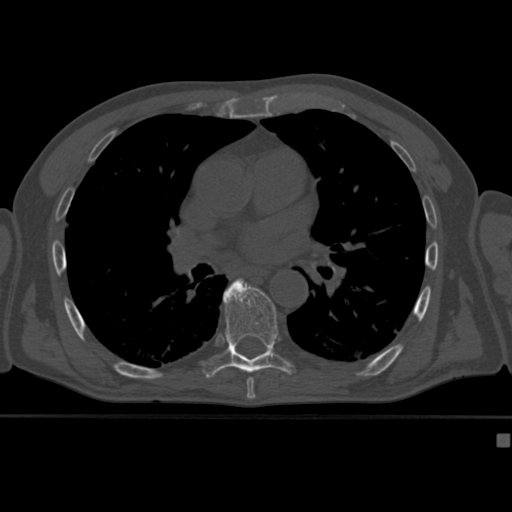
CT including the spine, one axial slice; position 266 of 430 along the scan axis; reconstruction kernel Br40s; 120 kVp; bone window (W 1800 / L 400 HU); 512 × 512 image matrix, field of view 337 × 337 mm. Patient: male, 64 years. Case-level facts recorded for this patient, not image findings: primary cancer: uterus.
Structures marked on this image (semi-automatically segmented with operator editing):
- T7 vertebra: box from (x=247, y=377) to (x=254, y=382) px
- T8 vertebra: (x=203, y=279)–(x=295, y=378)